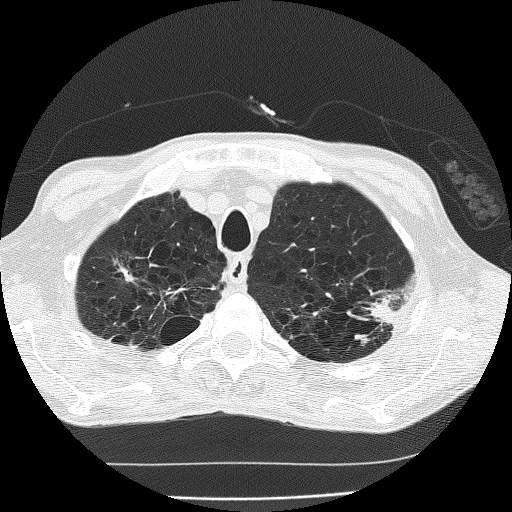
Axial slice from a low-dose chest CT screening exam. Second screening round (one year after baseline). Lung window (W 1500 / L -600 HU). 120 kVp. 512 × 512 image matrix, field of view 320 × 320 mm. Male, age 60 years at enrolment. Current smoker at enrolment.
Lesion marked by an expert reader, box from (x=346, y=278) to (x=416, y=342) px. The screening reader recorded 2 non-calcified nodules or masses ≥4 mm on this exam (left upper lobe, left upper lobe); which of them this box marks is not recorded. Official screen result: positive, other.